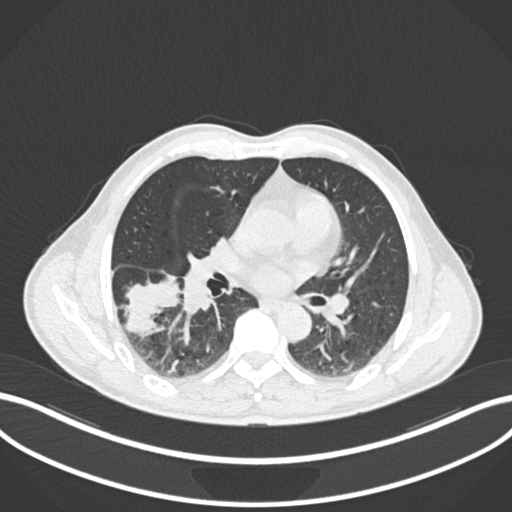
Chest CT, one axial slice; position 101 of 208 along the scan axis; reconstruction kernel B30f; 120 kVp; lung window (W 1500 / L -600 HU); 512 × 512 image matrix, field of view 400 × 400 mm. Patient: male, 58 years. Case-level facts recorded for this patient, not image findings: clinical TNM (as recorded): T3 N0 M0; histopathological grade: G2.
Annotated regions visible in this slice (bounding box drawn by a radiologist):
- lung tumour (recorded histology: squamous cell carcinoma): bounding box [x1, y1, x2, y2] px = [113, 261, 189, 345]